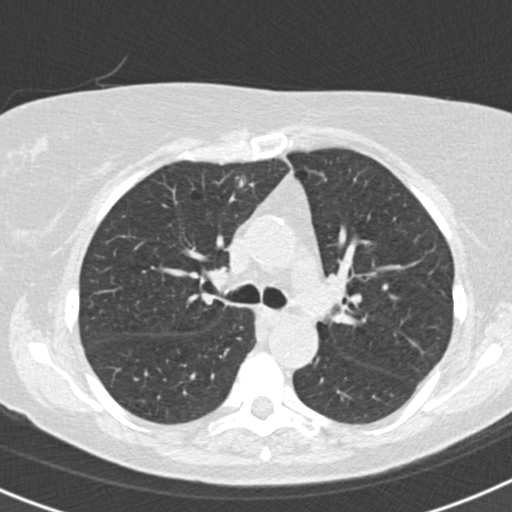
Chest CT (low-dose screening protocol), one axial image; second screening round (one year after baseline); lung window (W 1500 / L -600 HU); 2 mm slice thickness; standard (soft-tissue) reconstruction kernel (B30f); slice 56 of 160 in the series; 512 × 512 image matrix, field of view 306 × 306 mm. Female, age 72 years at enrolment. Former smoker at enrolment.
• Expert reader's lesion annotation, bounding box <216,162,261,206> (left, top, right, bottom; pixels).
• The exam's reader record, not a measurement of the box and not confirmed to be the same lesion: non-calcified nodule or mass ≥4 mm, right upper lobe, 5 × 5 mm, smooth margins, soft tissue attenuation.
• Official screen result: positive, other.
• Later outcome: lung cancer diagnosed 462 days after this screen (after the third annual screen) — adenocarcinoma, NOS, right upper lobe, moderately differentiated (G2), stage IA (AJCC 6th edition), 15 mm at pathology.